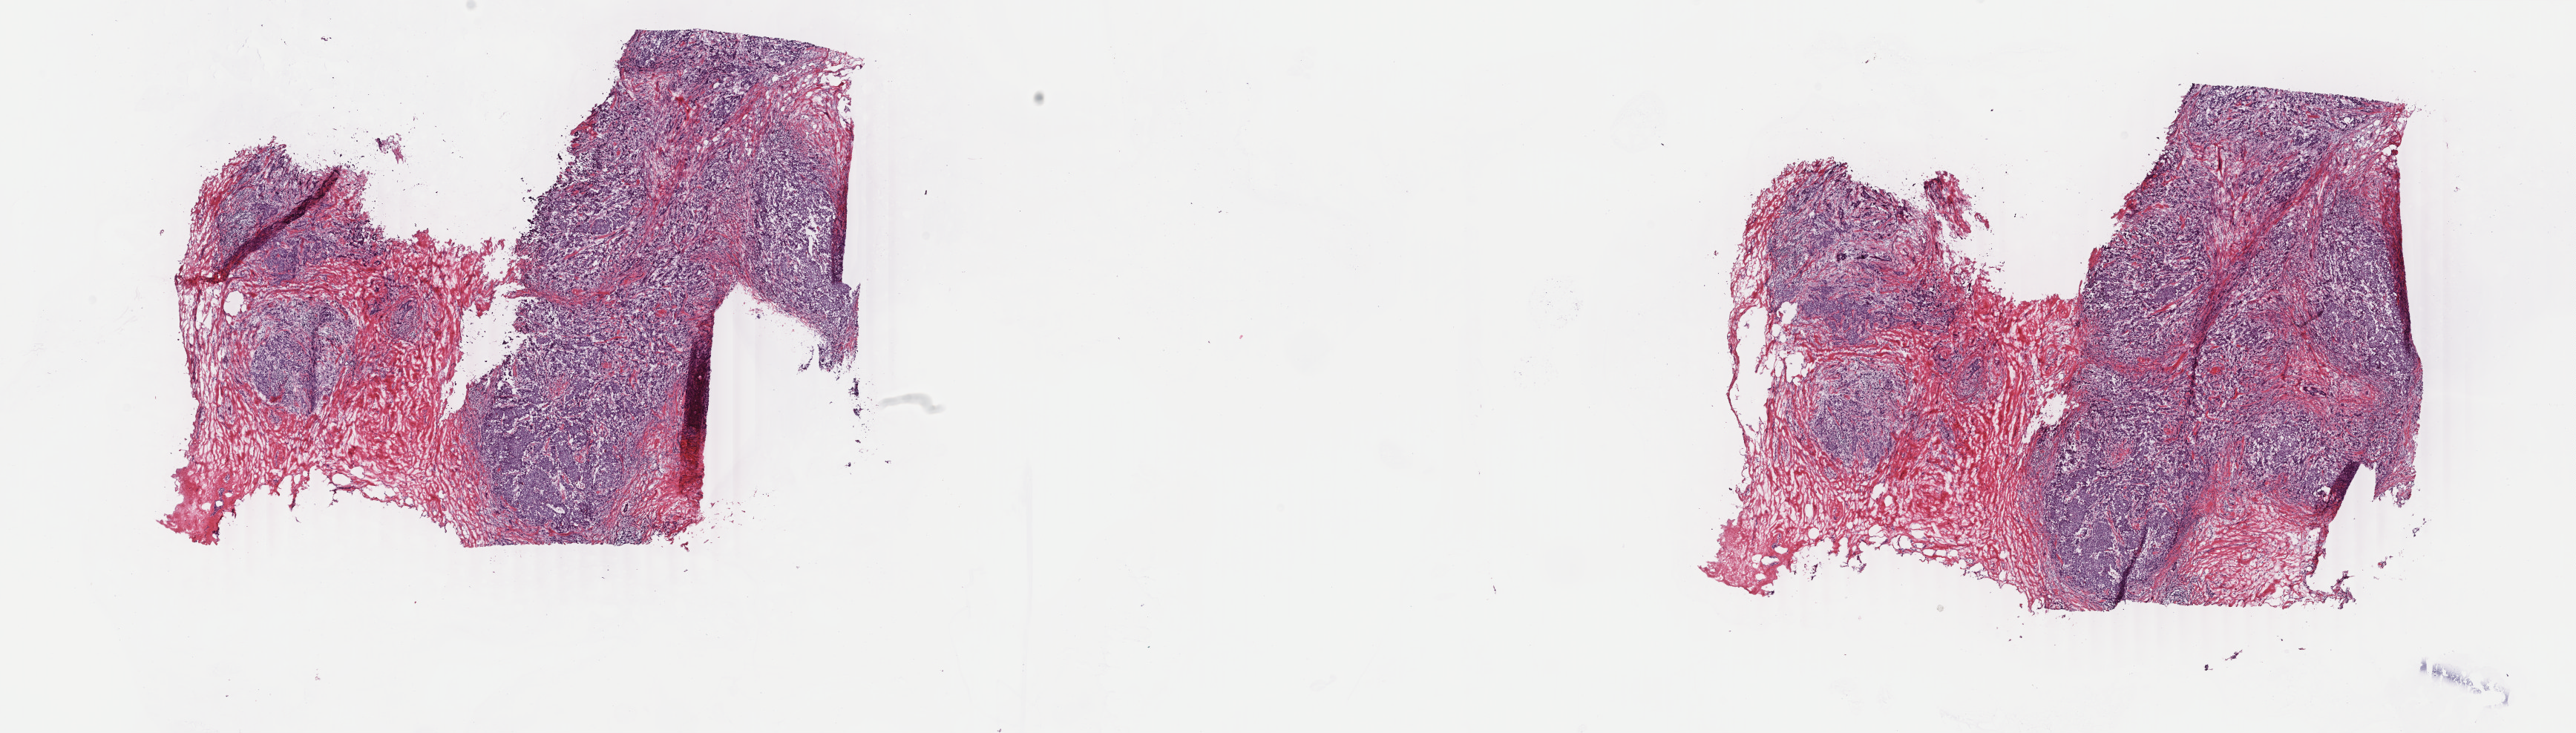
Whole-slide histology image, H&E-stained, shown as a low-resolution overview of the whole scanned area (about 27.6 x 7.9 mm, from a 40x scan); frozen section from the top of the tissue portion; breast, primary tumour sample. Female patient; age at initial diagnosis 59 years. Pathologist review of this section (percent, as recorded): tumour cells 70%, tumour nuclei 70%, normal cells 0%, stromal cells 20%, necrosis 10%. Infiltration values recorded for this section: lymphocyte infiltration 40%, monocyte infiltration 20%, neutrophil infiltration 20%.
• TNM: T2 N1a M0
• diagnosis: Infiltrating duct carcinoma, NOS
• lymph nodes positive (case pathology): 2 of 15 examined
• AJCC pathologic stage: IIB (7th edition)